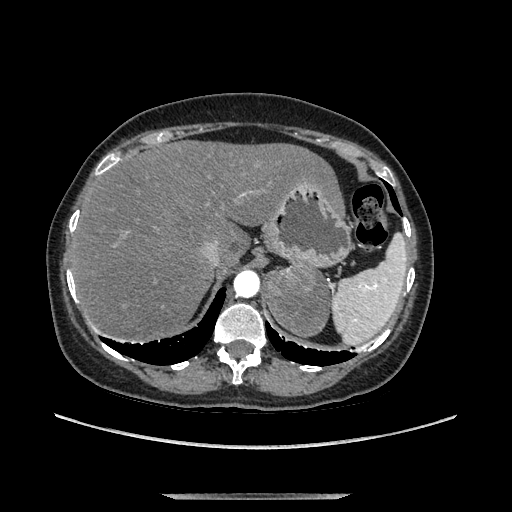
Contrast-enhanced abdominal CT, one axial slice. Slice 105 of 169 in the series (ordered by position). Soft-tissue window (W 400 / L 40 HU). 1.25 mm slice thickness. 512 × 512 image matrix, field of view 400 × 400 mm. Female patient. Case-level facts recorded for this patient, not image findings: diagnosis: adrenocortical carcinoma; tumour side: left adrenal; tumour size at pathology: 9 cm; Ki-67 index: 2 %; stage (as recorded): 3.
Outlined on this slice (semi-automatic segmentation, software-assisted and operator-edited):
- mass: bounding box (x1, y1, x2, y2) in pixels: (266, 266, 328, 334)